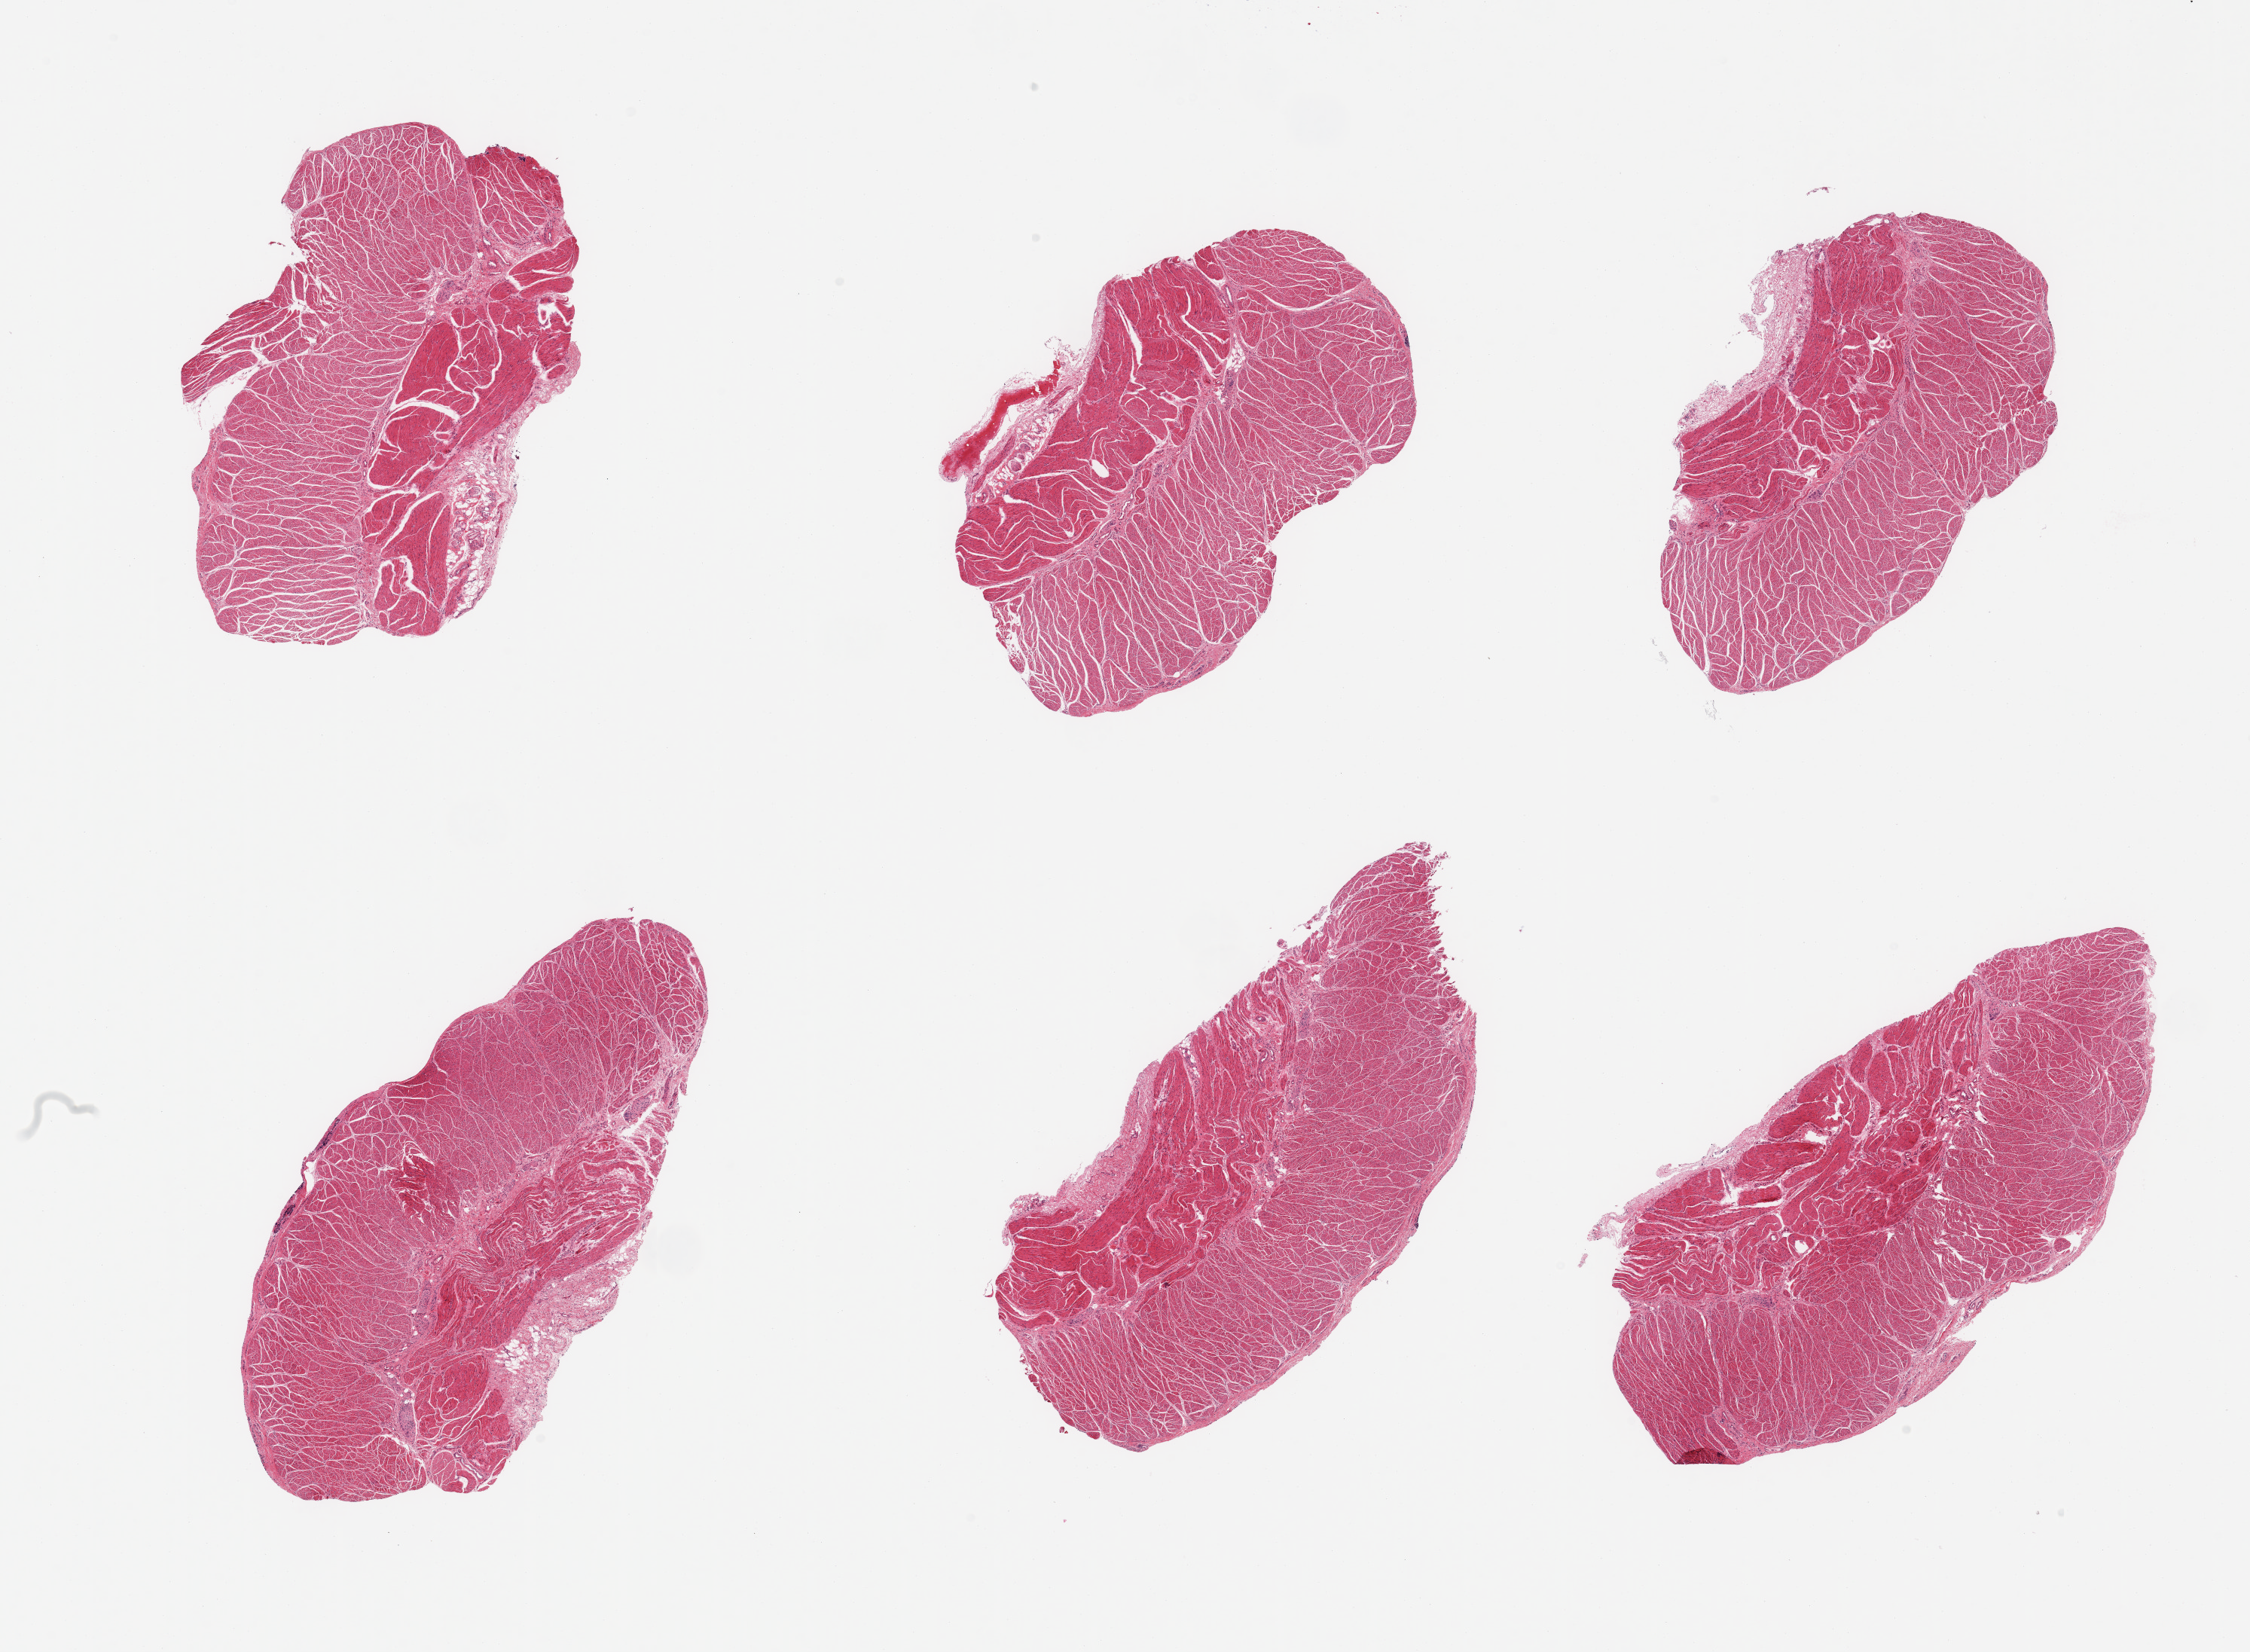
Digitized H&E-stained section, brightfield — a low-resolution overview of the entire scanned area, about 23.6 x 17.3 mm, PAXgene-fixed paraffin-embedded (PFPE) section, section of esophageal muscle (target tissue), tissue donor sample. Donor: female.
• reviewer comment on this tissue sample: 6 pieces; target muscularis